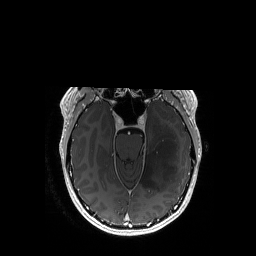
Brain MRI from a brain-tumour surgery series, one axial slice. Position 113 of 192 along the scan axis. T1-weighted post-contrast. 1 mm slice thickness. 256 × 256 image matrix. Case-level facts recorded for this patient, not image findings: histopathology: Astrocytoma; WHO grade: 3; IDH mutation: yes.
Outlined on this slice (manually delineated by an expert):
- tumour: bounding box (x1, y1, x2, y2) in pixels: (140, 116, 178, 191)